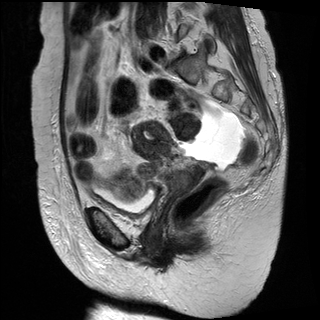
Pelvic MRI for cervical cancer, one sagittal slice. Slice 18 of 30 in the series (ordered by position). T2-weighted. 1.5 T. TE 89 ms, TR 2930 ms. 4 mm slice thickness. 320 × 320 image matrix. Patient: female, 61 years.
Structures marked on this image (expert manual segmentation):
- uterus and cervix: bounding box [x1, y1, x2, y2] px = [130, 121, 209, 198]